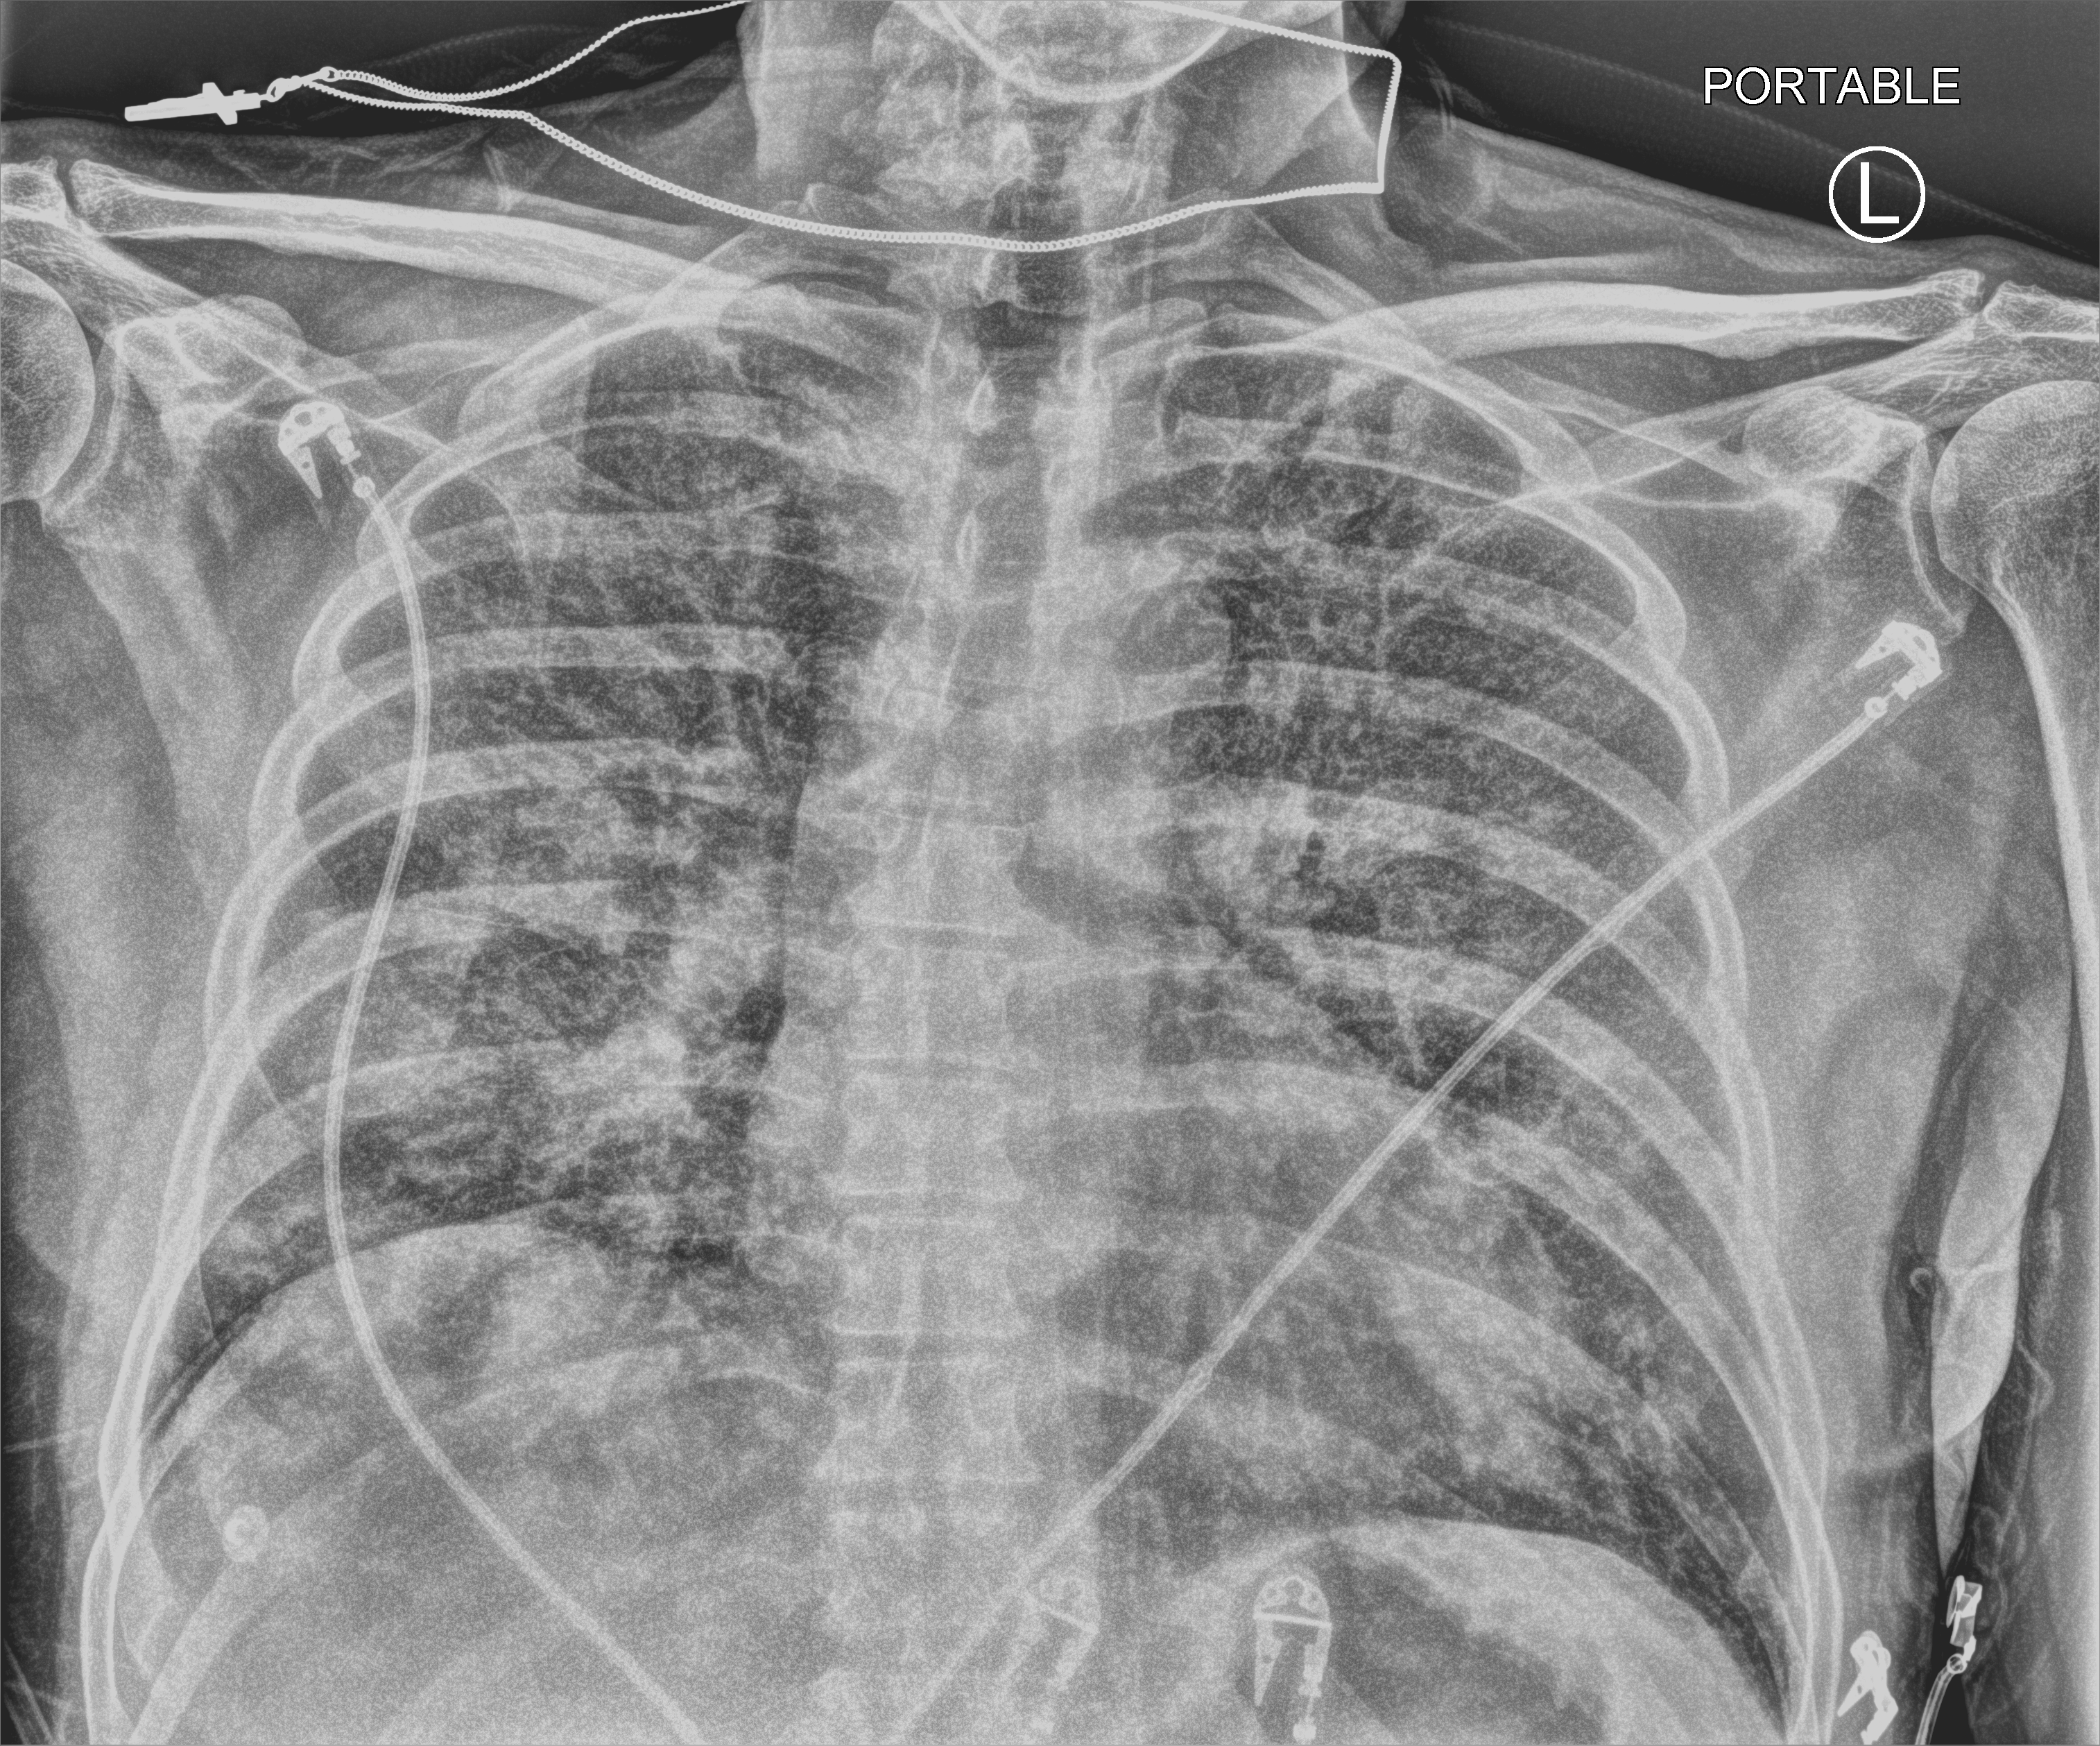
Portable chest radiograph; anteroposterior (AP) projection. Male patient hospitalised with COVID-19, age 60–74 years.
Admission-level facts for this patient (not findings on this image; timing relative to this image not recorded):
- admitted to intensive care during this hospital stay: no